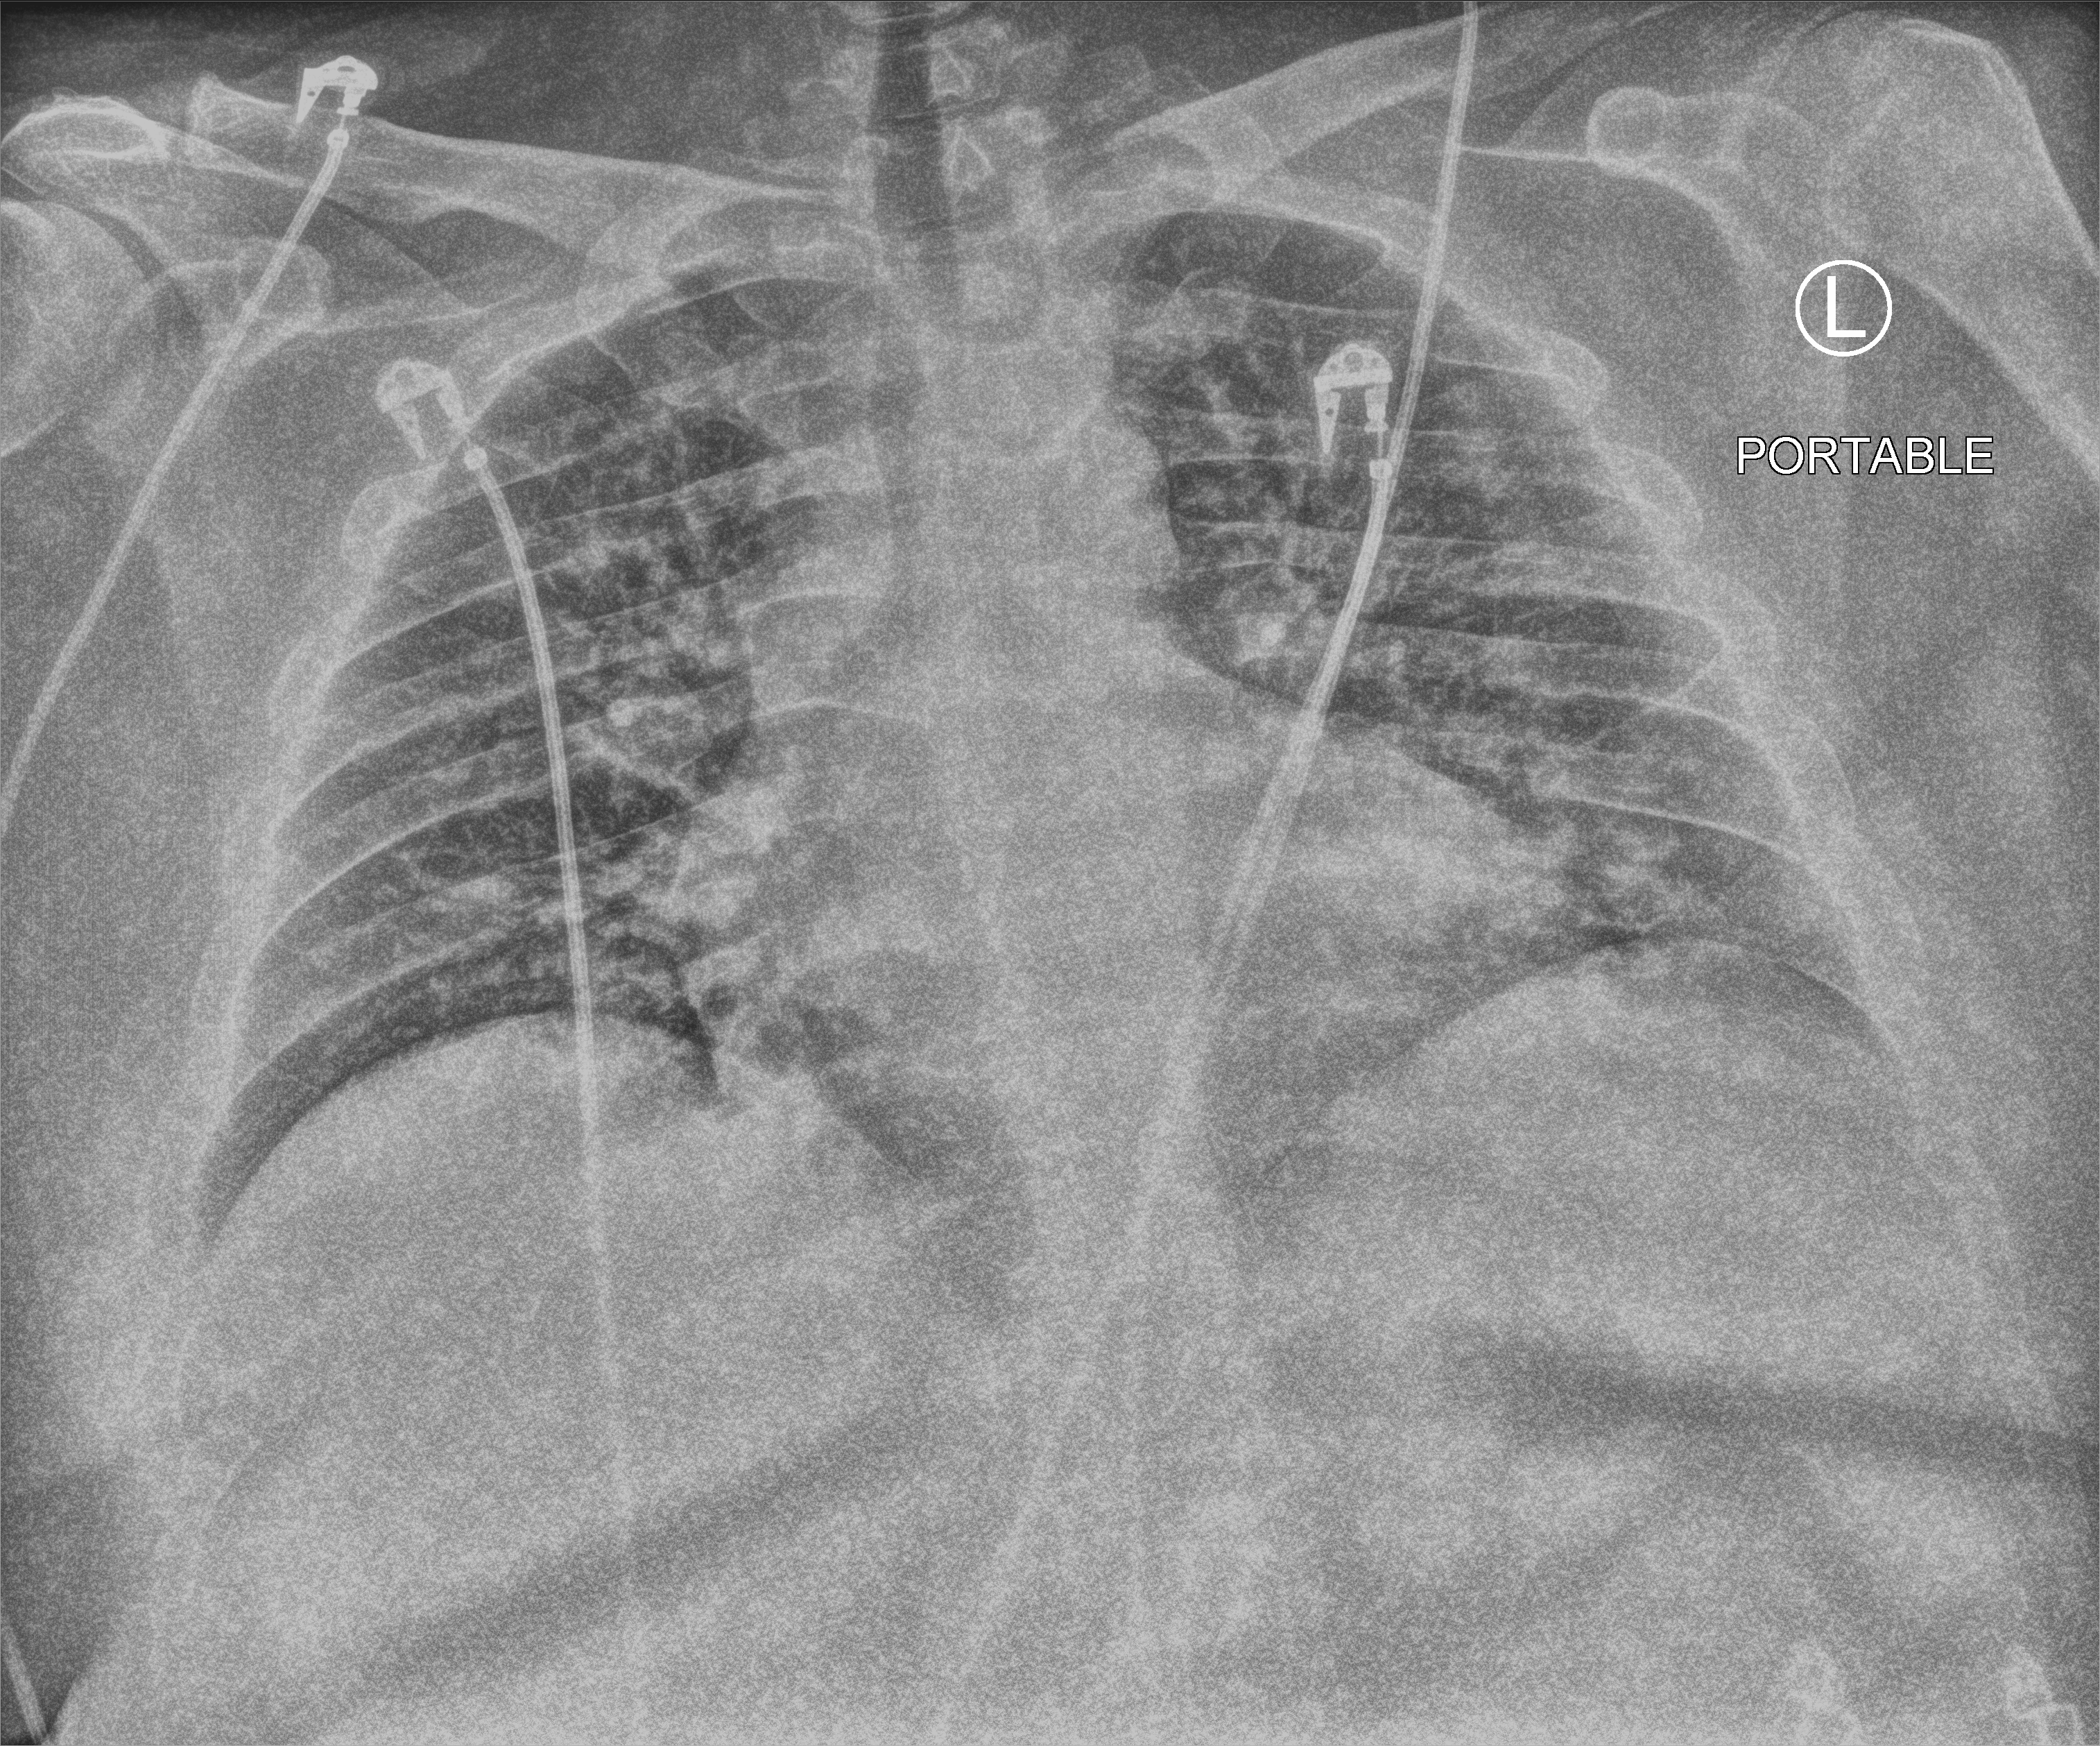
Portable chest radiograph. Patient hospitalised with COVID-19; male, aged 18–59 years.
From the hospital-stay record, not from the radiograph (when in the stay this image was taken is not recorded): admitted to intensive care during this hospital stay: no; other chronic lung disease (admission record): no; mechanically ventilated during this hospital stay: no.